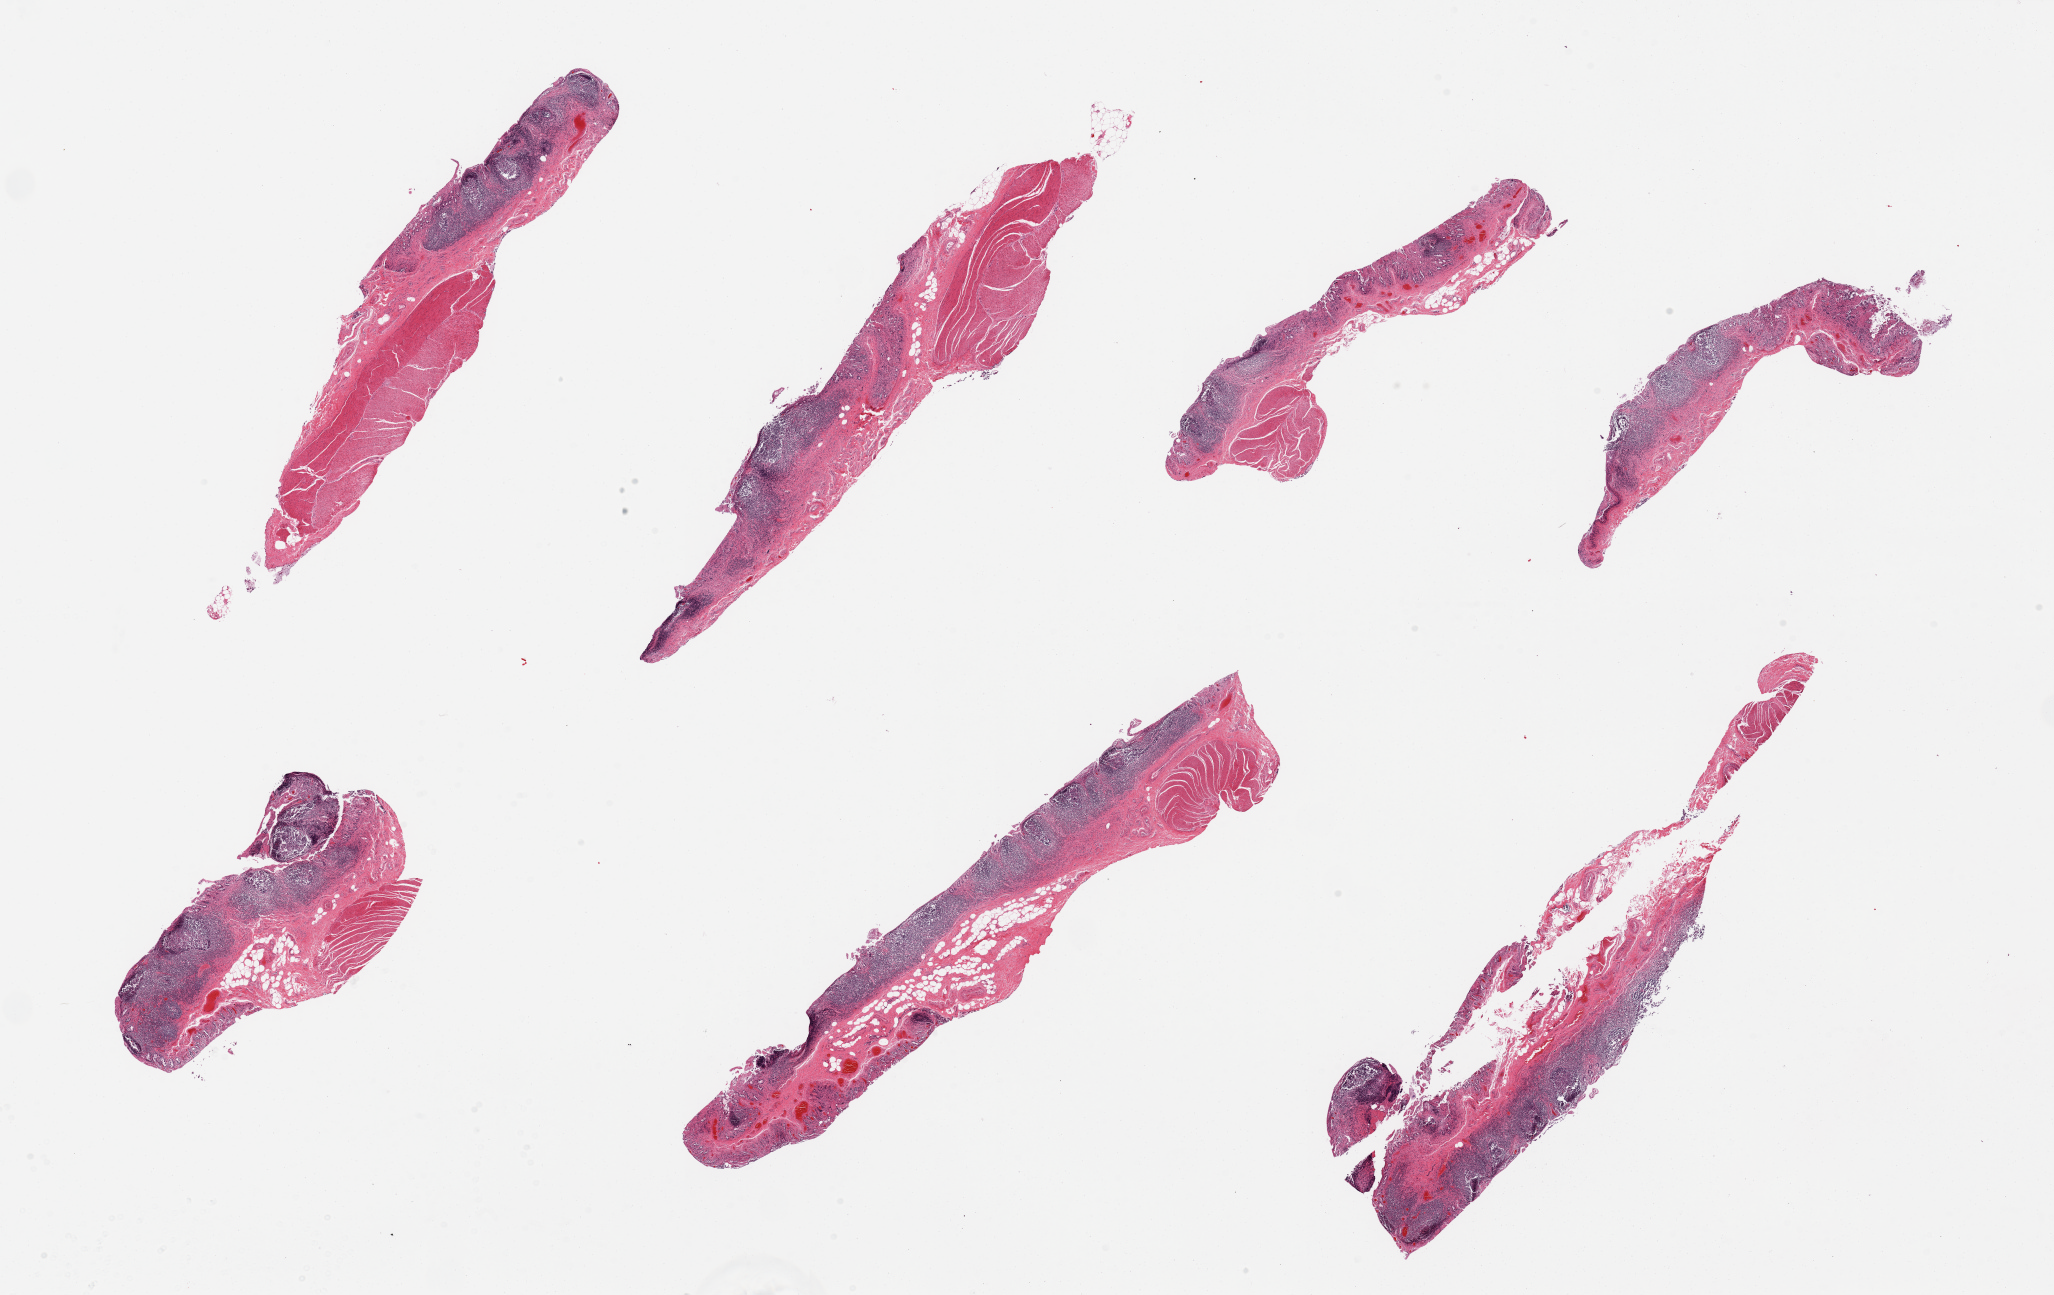
Digitized H&E-stained section — low-resolution overview of the scanned area, about 32.5 x 20.5 mm (slide scanned at 20x), PAXgene-fixed, paraffin-embedded tissue, target tissue: ileum, tissue donor sample. Donor: male.
Review note (as recorded): 7 pieces, markedly autolyzed mucosa with abundant lymphoid tissue, muscularis.